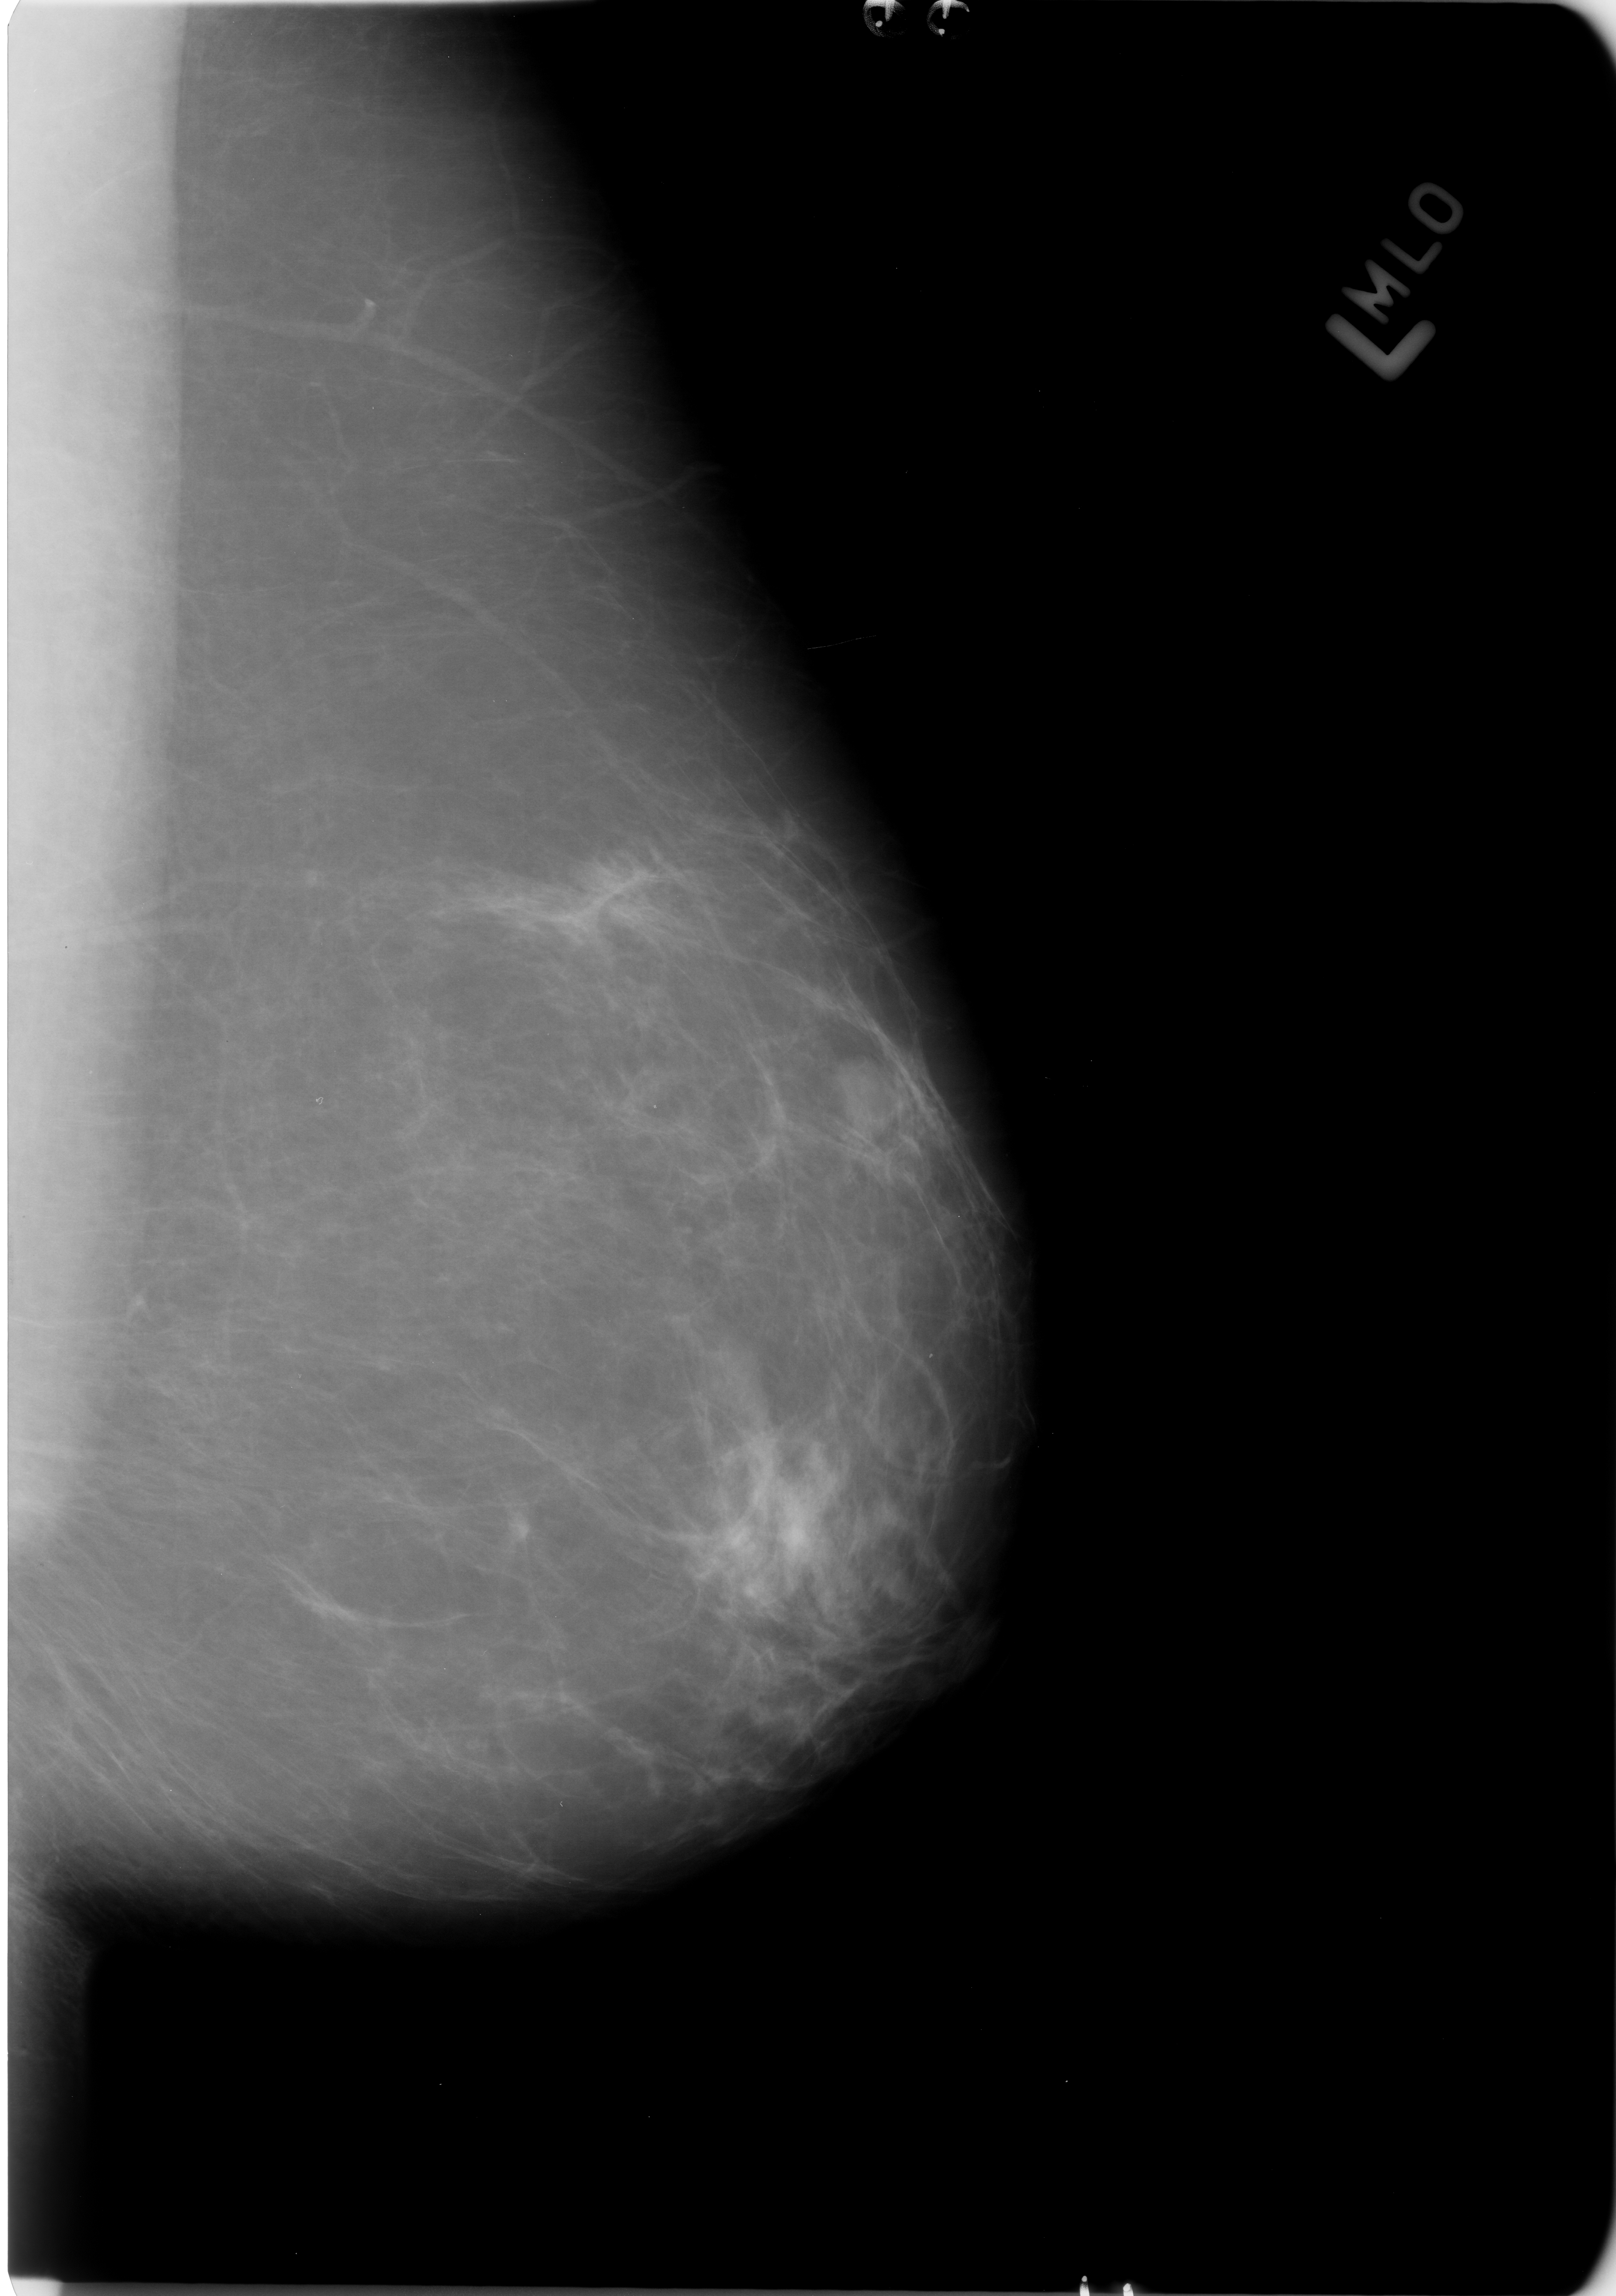
Digitized screen-film mammogram; left breast; MLO view; breast composition: scattered fibroglandular densities (BI-RADS density category 2 of 4); 1616 × 2296 image matrix.
Expert-marked regions of interest on this film, with their recorded descriptors:
- mass, shape lobulated, margins circumscribed; BI-RADS assessment category 3; pathology result (as recorded, not read from the image): benign: bounding box [x1, y1, x2, y2] px = [825, 1052, 892, 1146]